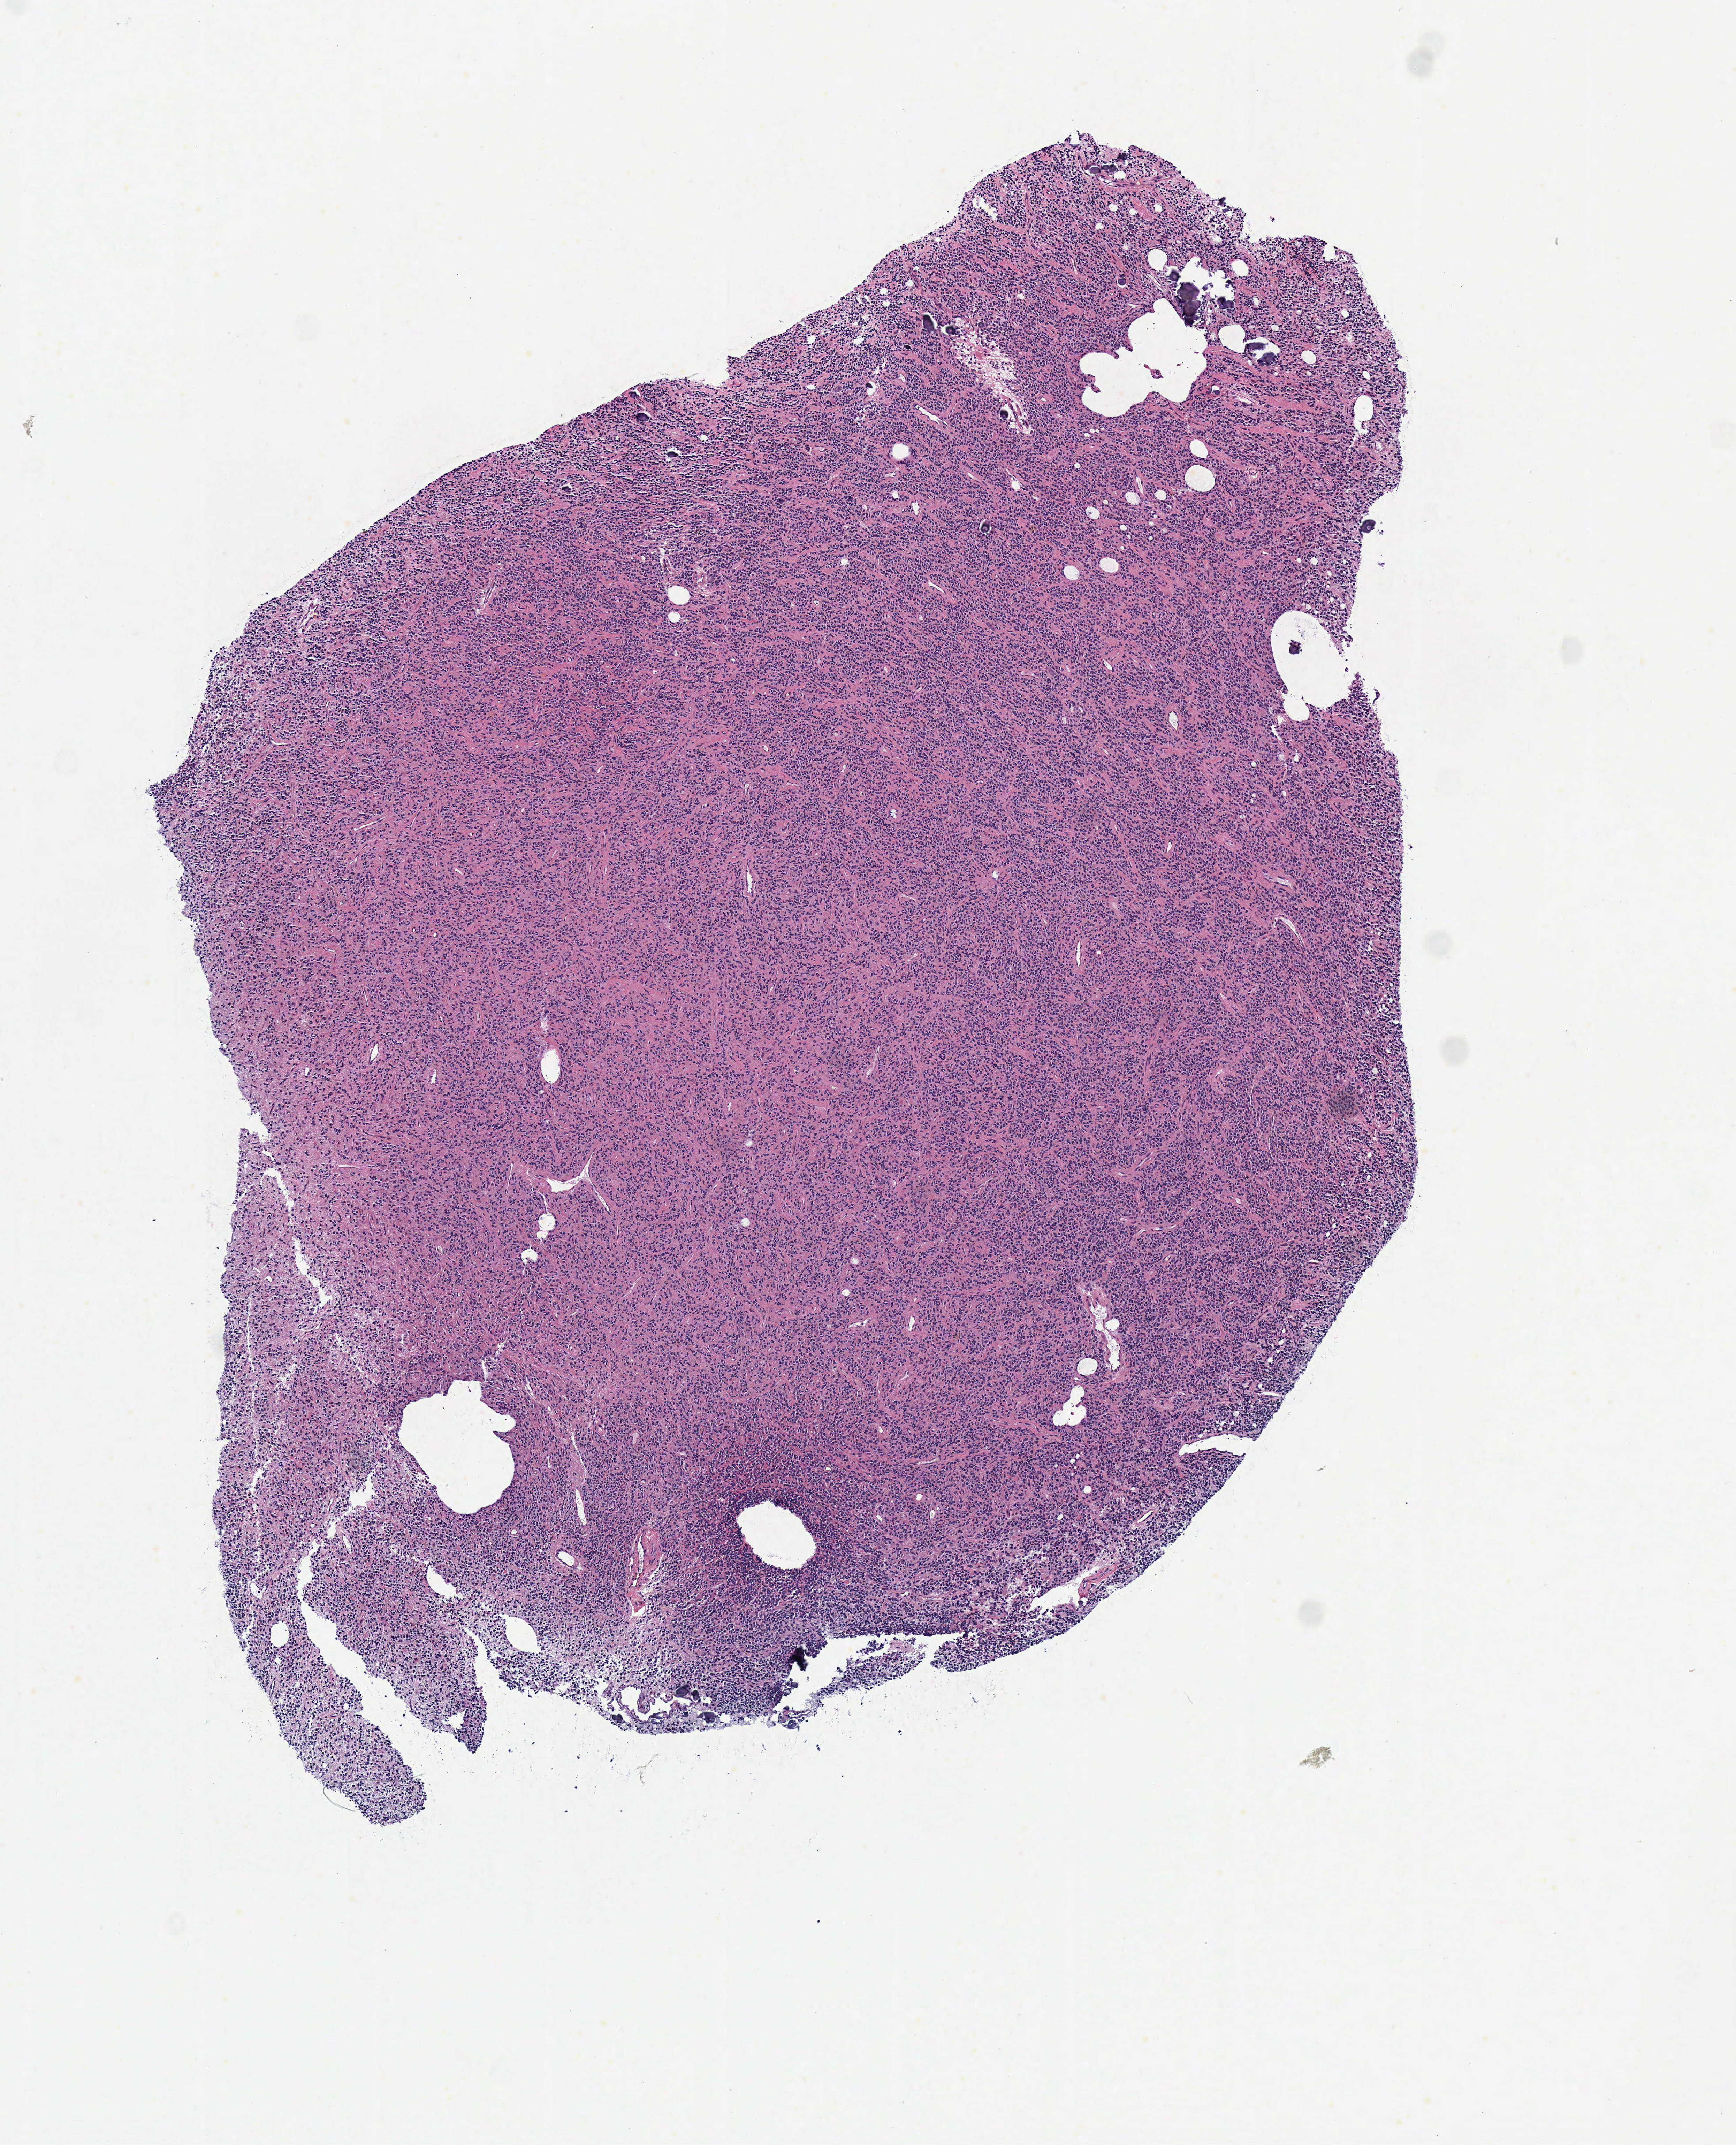
Whole-slide histology image, H&E-stained — low-resolution overview of the scanned area, about 4.9 x 6.0 mm (acquisition: 40x scan); frozen section; primary tumour sample from the brain. Male, age 53 years at initial diagnosis. Pathologist review of this section (percent, as recorded): tumour cells 100%, tumour nuclei 85%.
Histologic diagnosis: Oligodendroglioma, anaplastic (cerebrum).